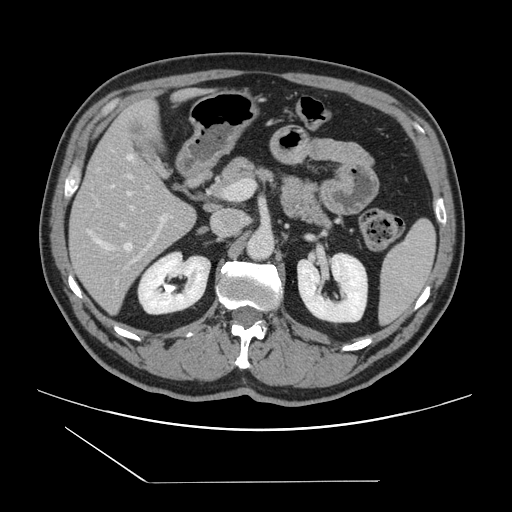
Contrast-enhanced abdominal CT, one axial slice; slice 74 of 157 in the series (ordered by position); intravenous contrast given; soft-tissue window (W 400 / L 40 HU); 2.5 mm slice thickness; 512 × 512 image matrix, field of view 407 × 407 mm. Male patient, age 61 years. From the clinical record (not read from this slice): diagnosis: colorectal cancer liver metastases, imaged before liver resection; multiple liver metastases: yes; largest metastasis: 5.5 cm; chemotherapy before resection: no.
Annotated regions visible in this slice (manually delineated by an expert):
- hepatic veins: bounding box [x1, y1, x2, y2] px = [88, 154, 133, 250]
- liver: [71, 102, 195, 312]
- planned liver remnant (the part of the liver to remain after resection): [72, 102, 181, 220]
- portal vein (with intrahepatic branches): [121, 174, 167, 261]